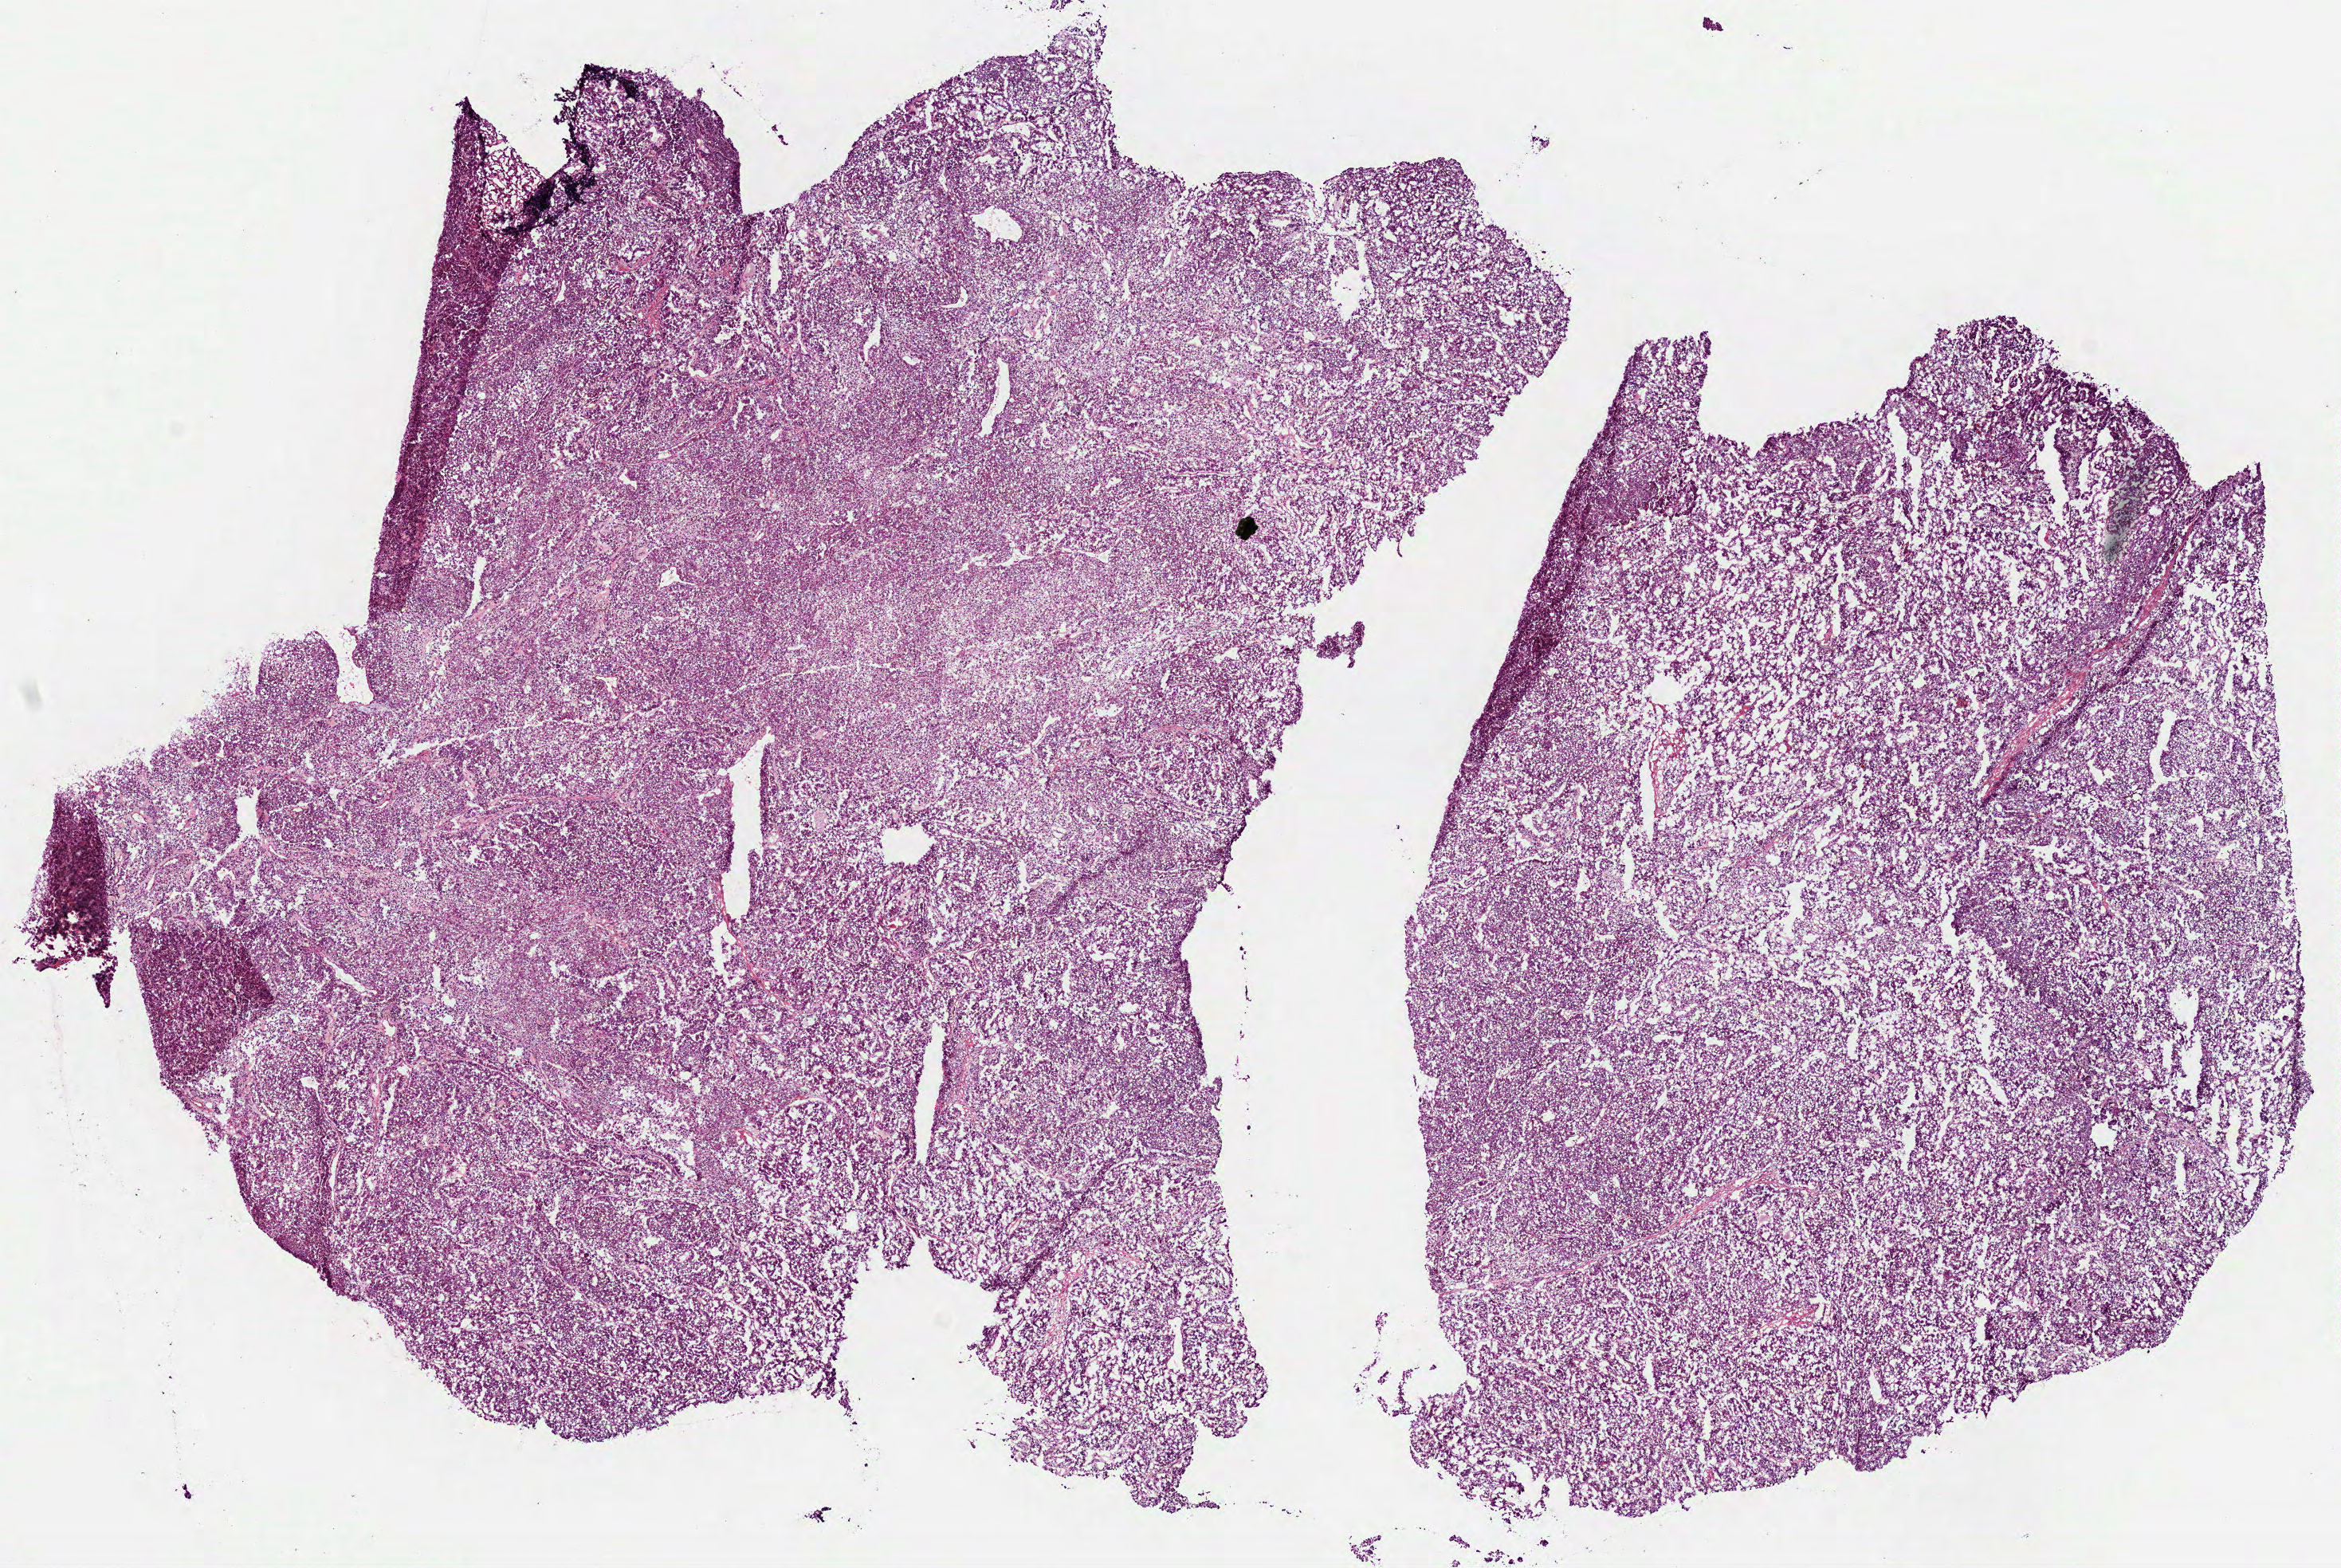
H&E-stained whole-slide image, whole scanned area (about 11.8 x 7.9 mm) shown as a low-resolution overview. Frozen section. Sample: primary tumour, kidney. Patient: female, age at initial diagnosis 55 years. Pathologist review of this section (percent, as recorded): tumour cells 100%, tumour nuclei 80%.
Diagnosis: Papillary adenocarcinoma, NOS.